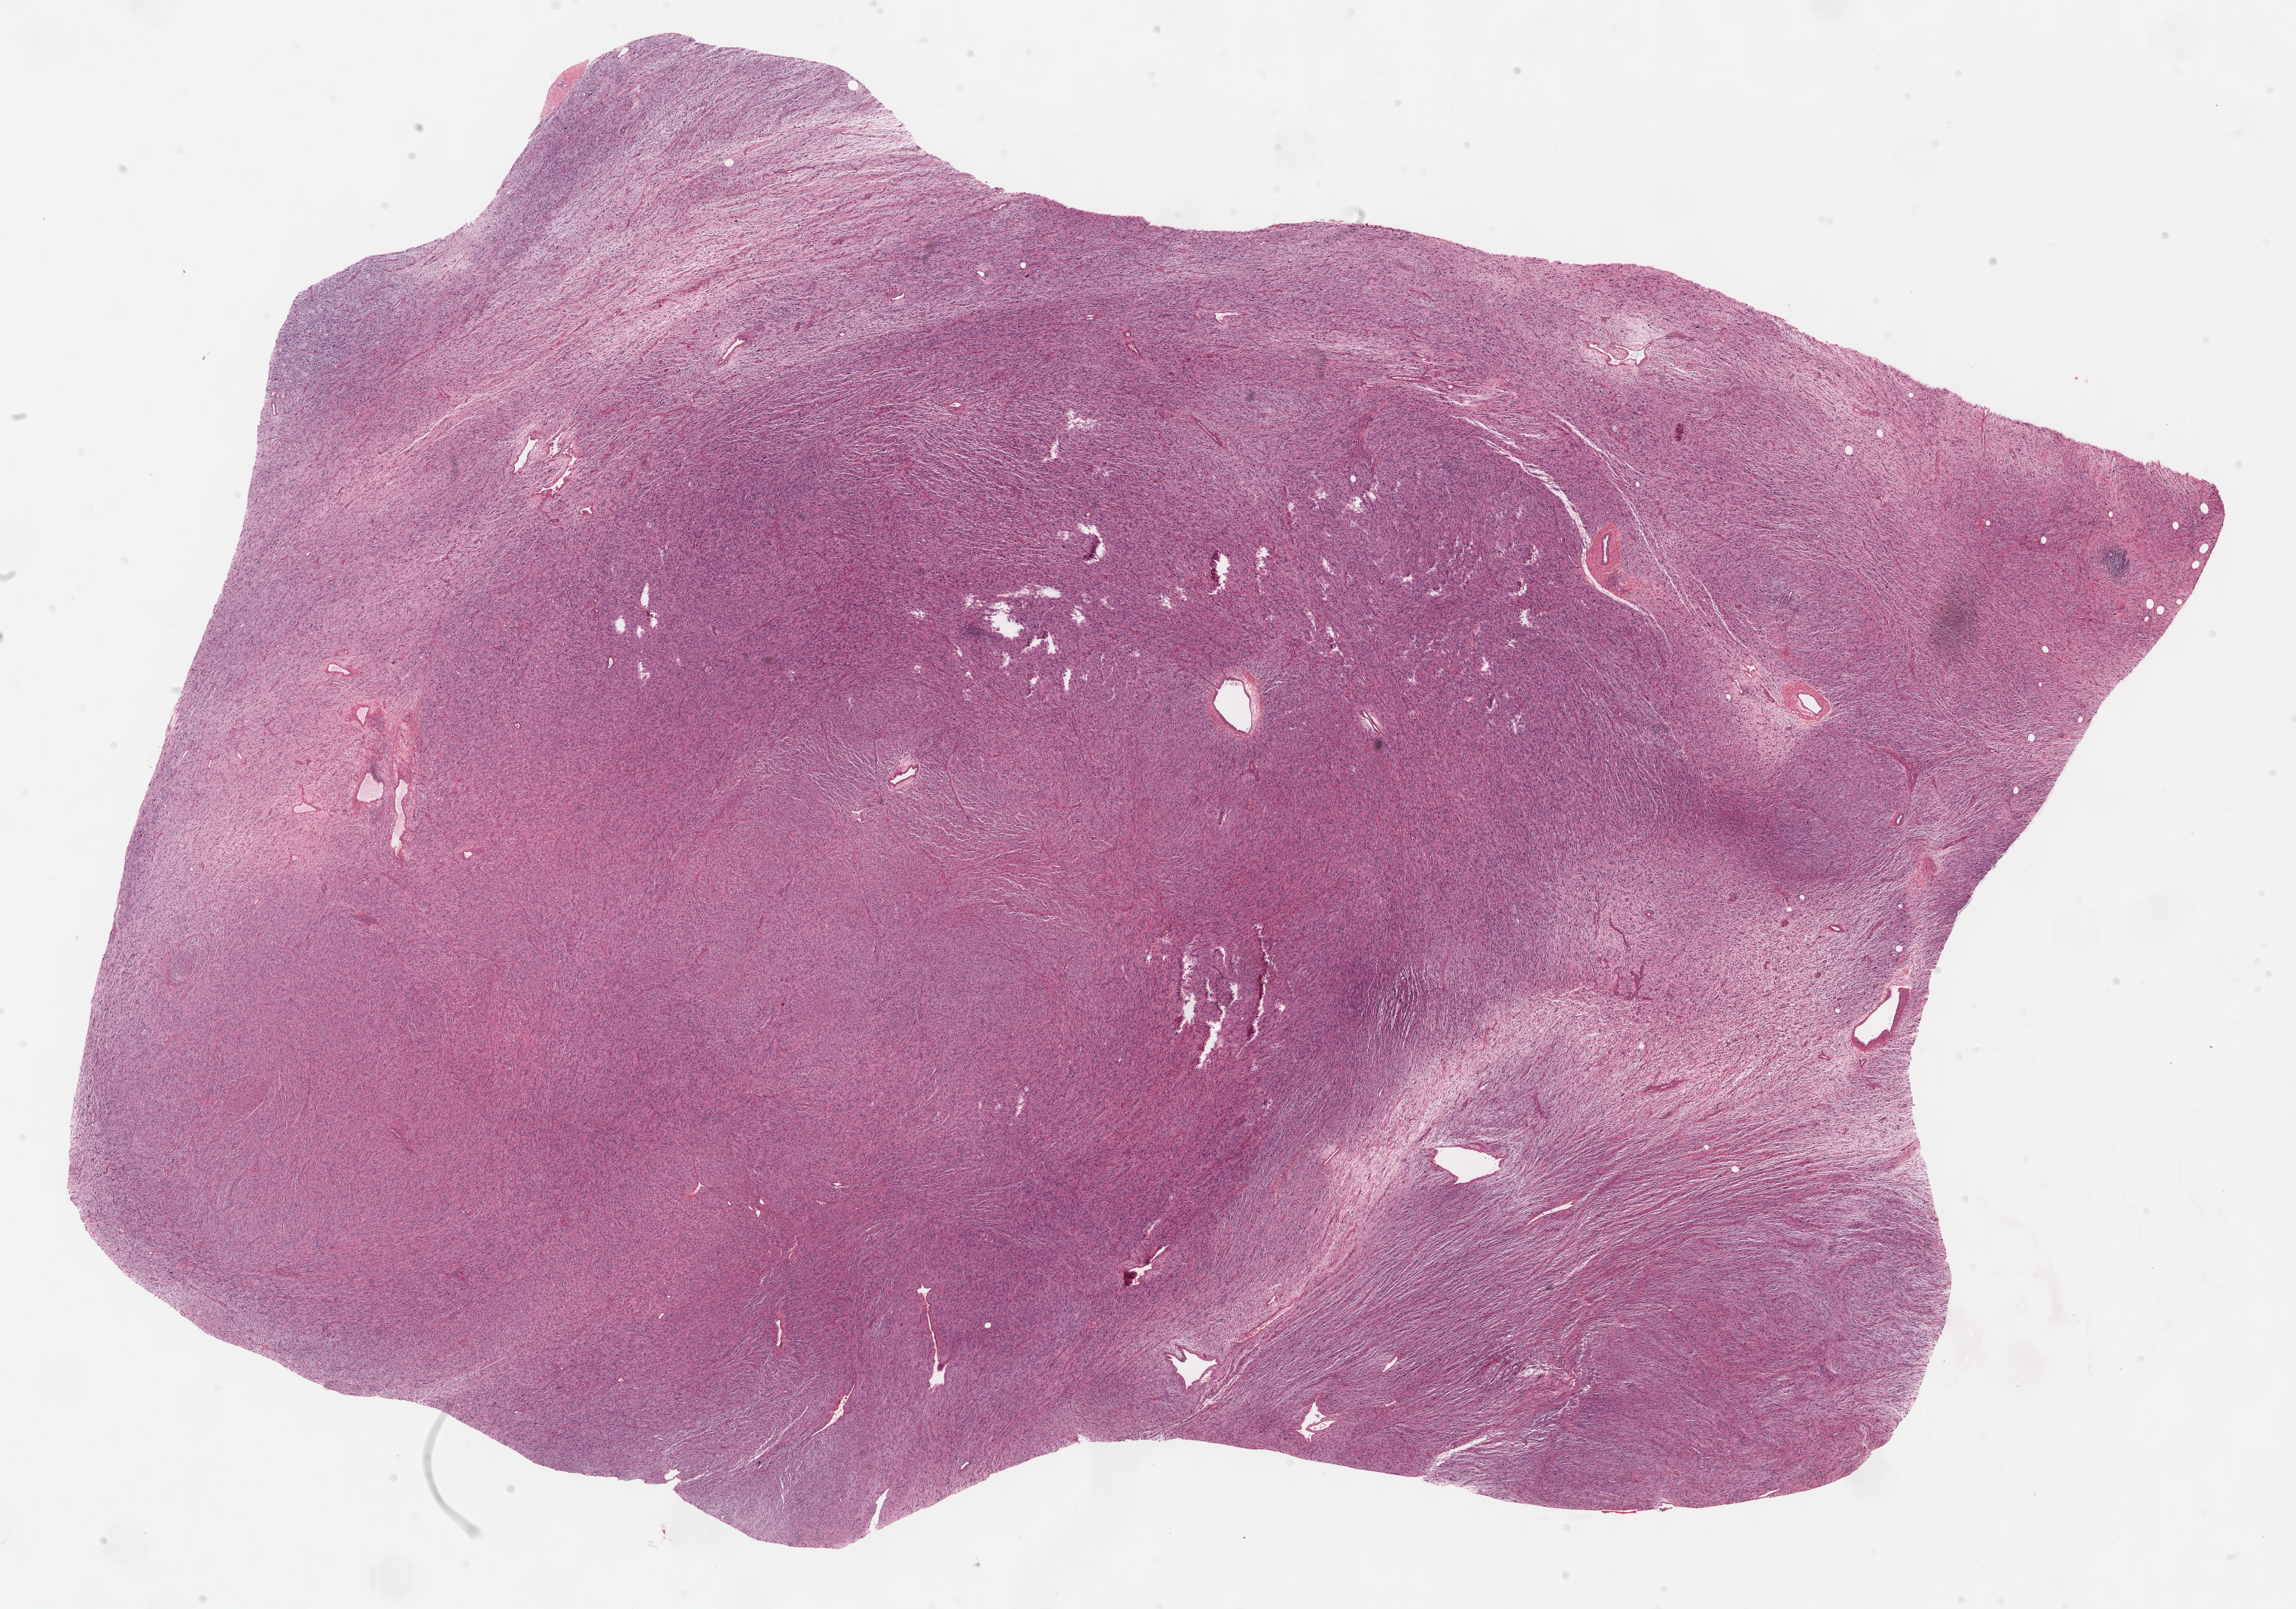
Digitized H&E tissue section (whole slide), low-resolution overview of the scanned area, about 24.7 x 17.3 mm, formalin-fixed paraffin-embedded (FFPE) diagnostic section, connective, subcutaneous and other soft tissues, primary tumour sample. Male, age 59 years at initial diagnosis.
* histologic diagnosis: Fibromyxosarcoma